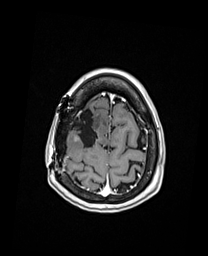
Brain MRI from a brain-tumour surgery series, one axial slice. Position 36 of 192 along the scan axis. T1-weighted post-contrast. 1 mm slice thickness. 208 × 256 image matrix, field of view 208 × 256 mm. Case-level facts recorded for this patient, not image findings: histopathology: Oligodendroglioma; WHO grade: 3; IDH mutation: yes; tumour location: Right Frontal.
Outlined on this slice (outlined manually by an expert reader):
- previous resection cavity: bounding box <72,109,99,148> (left, top, right, bottom; pixels)